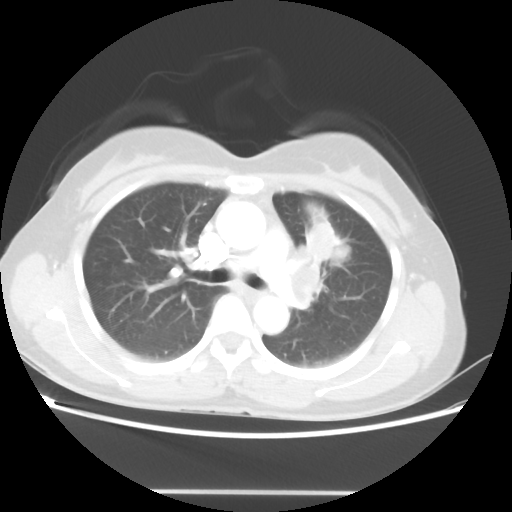
Chest CT, one axial slice. Position 29 of 46 along the scan axis. Reconstruction kernel STANDARD. Lung window (W 1500 / L -600 HU). 5 mm slice thickness. 512 × 512 image matrix, field of view 360 × 360 mm. Patient: female, 50 years. From the clinical record (not read from this slice): clinical TNM (as recorded): T1c N1 M0.
Annotated regions visible in this slice (bounding box drawn by a radiologist):
- lung tumour (recorded histology: adenocarcinoma): bounding box [x1, y1, x2, y2] px = [302, 220, 341, 262]